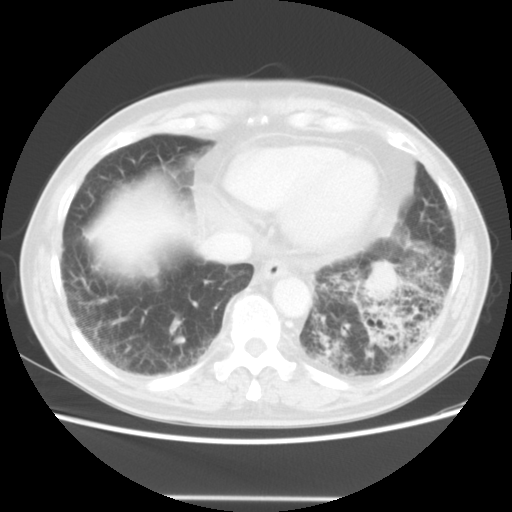
Chest CT, one axial slice. Position 12 of 56 along the scan axis. Reconstruction kernel STANDARD. 140 kVp. Lung window (W 1500 / L -600 HU). 512 × 512 image matrix, field of view 360 × 360 mm. Patient: male, 66 years. Case-level facts recorded for this patient, not image findings: clinical TNM (as recorded): T4 N3 M0; histopathological grade: G3.
Annotated regions visible in this slice (rectangle marked by the reading radiologist):
- lung tumour (recorded histology: small cell carcinoma): bounding box [x1, y1, x2, y2] px = [361, 259, 402, 312]